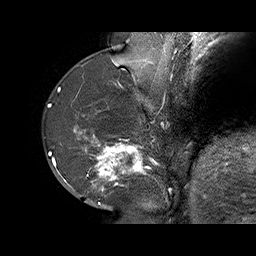
Breast MRI (dynamic contrast-enhanced), one sagittal slice; position 22 of 70 along the scan axis; dynamic contrast-enhanced series, time point 2 of 6 at this slice position (early post-contrast); 1.5 T; TE 4.5 ms, TR 32.4 ms; 3 mm slice thickness; 256 × 256 image matrix, field of view 180 × 180 mm. Female patient. Case-level facts recorded for this patient, not image findings: setting: breast cancer imaged before/during neoadjuvant chemotherapy; receptor status: HR-positive, HER2-negative.
Structures marked on this image (semi-automatically segmented with operator editing):
- analysis volume of interest (the breast-tissue region the enhancement analysis was run in; not a lesion): bounding box (x1, y1, x2, y2) in pixels: (71, 128, 159, 202)
- tumour enhancement mask (voxels above the 100 % enhancement threshold inside the analysis volume of interest): (73, 128, 147, 191)